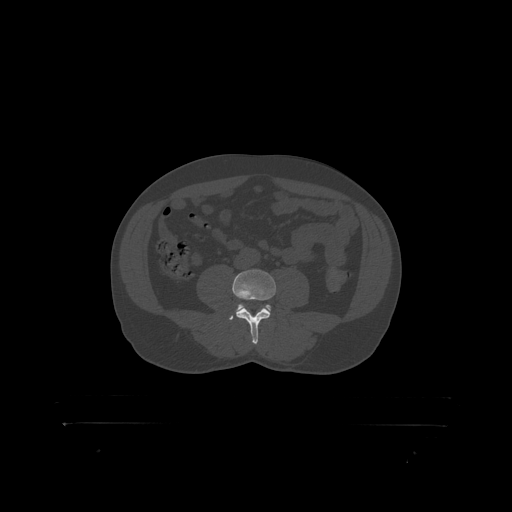
CT including the spine, one axial slice. Slice 227 of 399 in the series (ordered by position). Bone window (W 1800 / L 400 HU). 1.25 mm slice thickness. 512 × 512 image matrix. Patient: male, 46 years. Case-level facts recorded for this patient, not image findings: primary cancer: skin.
Annotated regions visible in this slice (semi-automatic segmentation, software-assisted and operator-edited):
- L4 vertebra: box from (x=233, y=270) to (x=277, y=319) px
- L5 vertebra: (x=237, y=305)–(x=271, y=311)